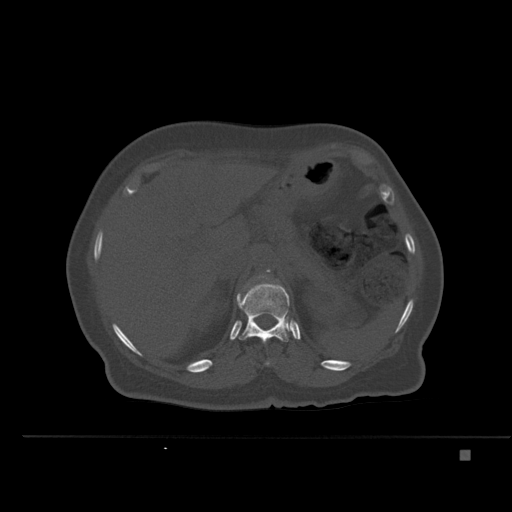
CT including the spine, one axial slice. Slice 253 of 477 in the series (ordered by position). Bone window (W 1800 / L 400 HU). 1.5 mm slice thickness. 512 × 512 image matrix, field of view 422 × 422 mm. Female patient, age 74 years. Case-level facts recorded for this patient, not image findings: primary cancer: colon.
Structures marked on this image (semi-automatically segmented with operator editing):
- L1 vertebra: box from (x=240, y=275) to (x=278, y=297) px
- T11 vertebra: (x=265, y=361)–(x=270, y=366)
- T12 vertebra: (x=236, y=281)–(x=292, y=343)